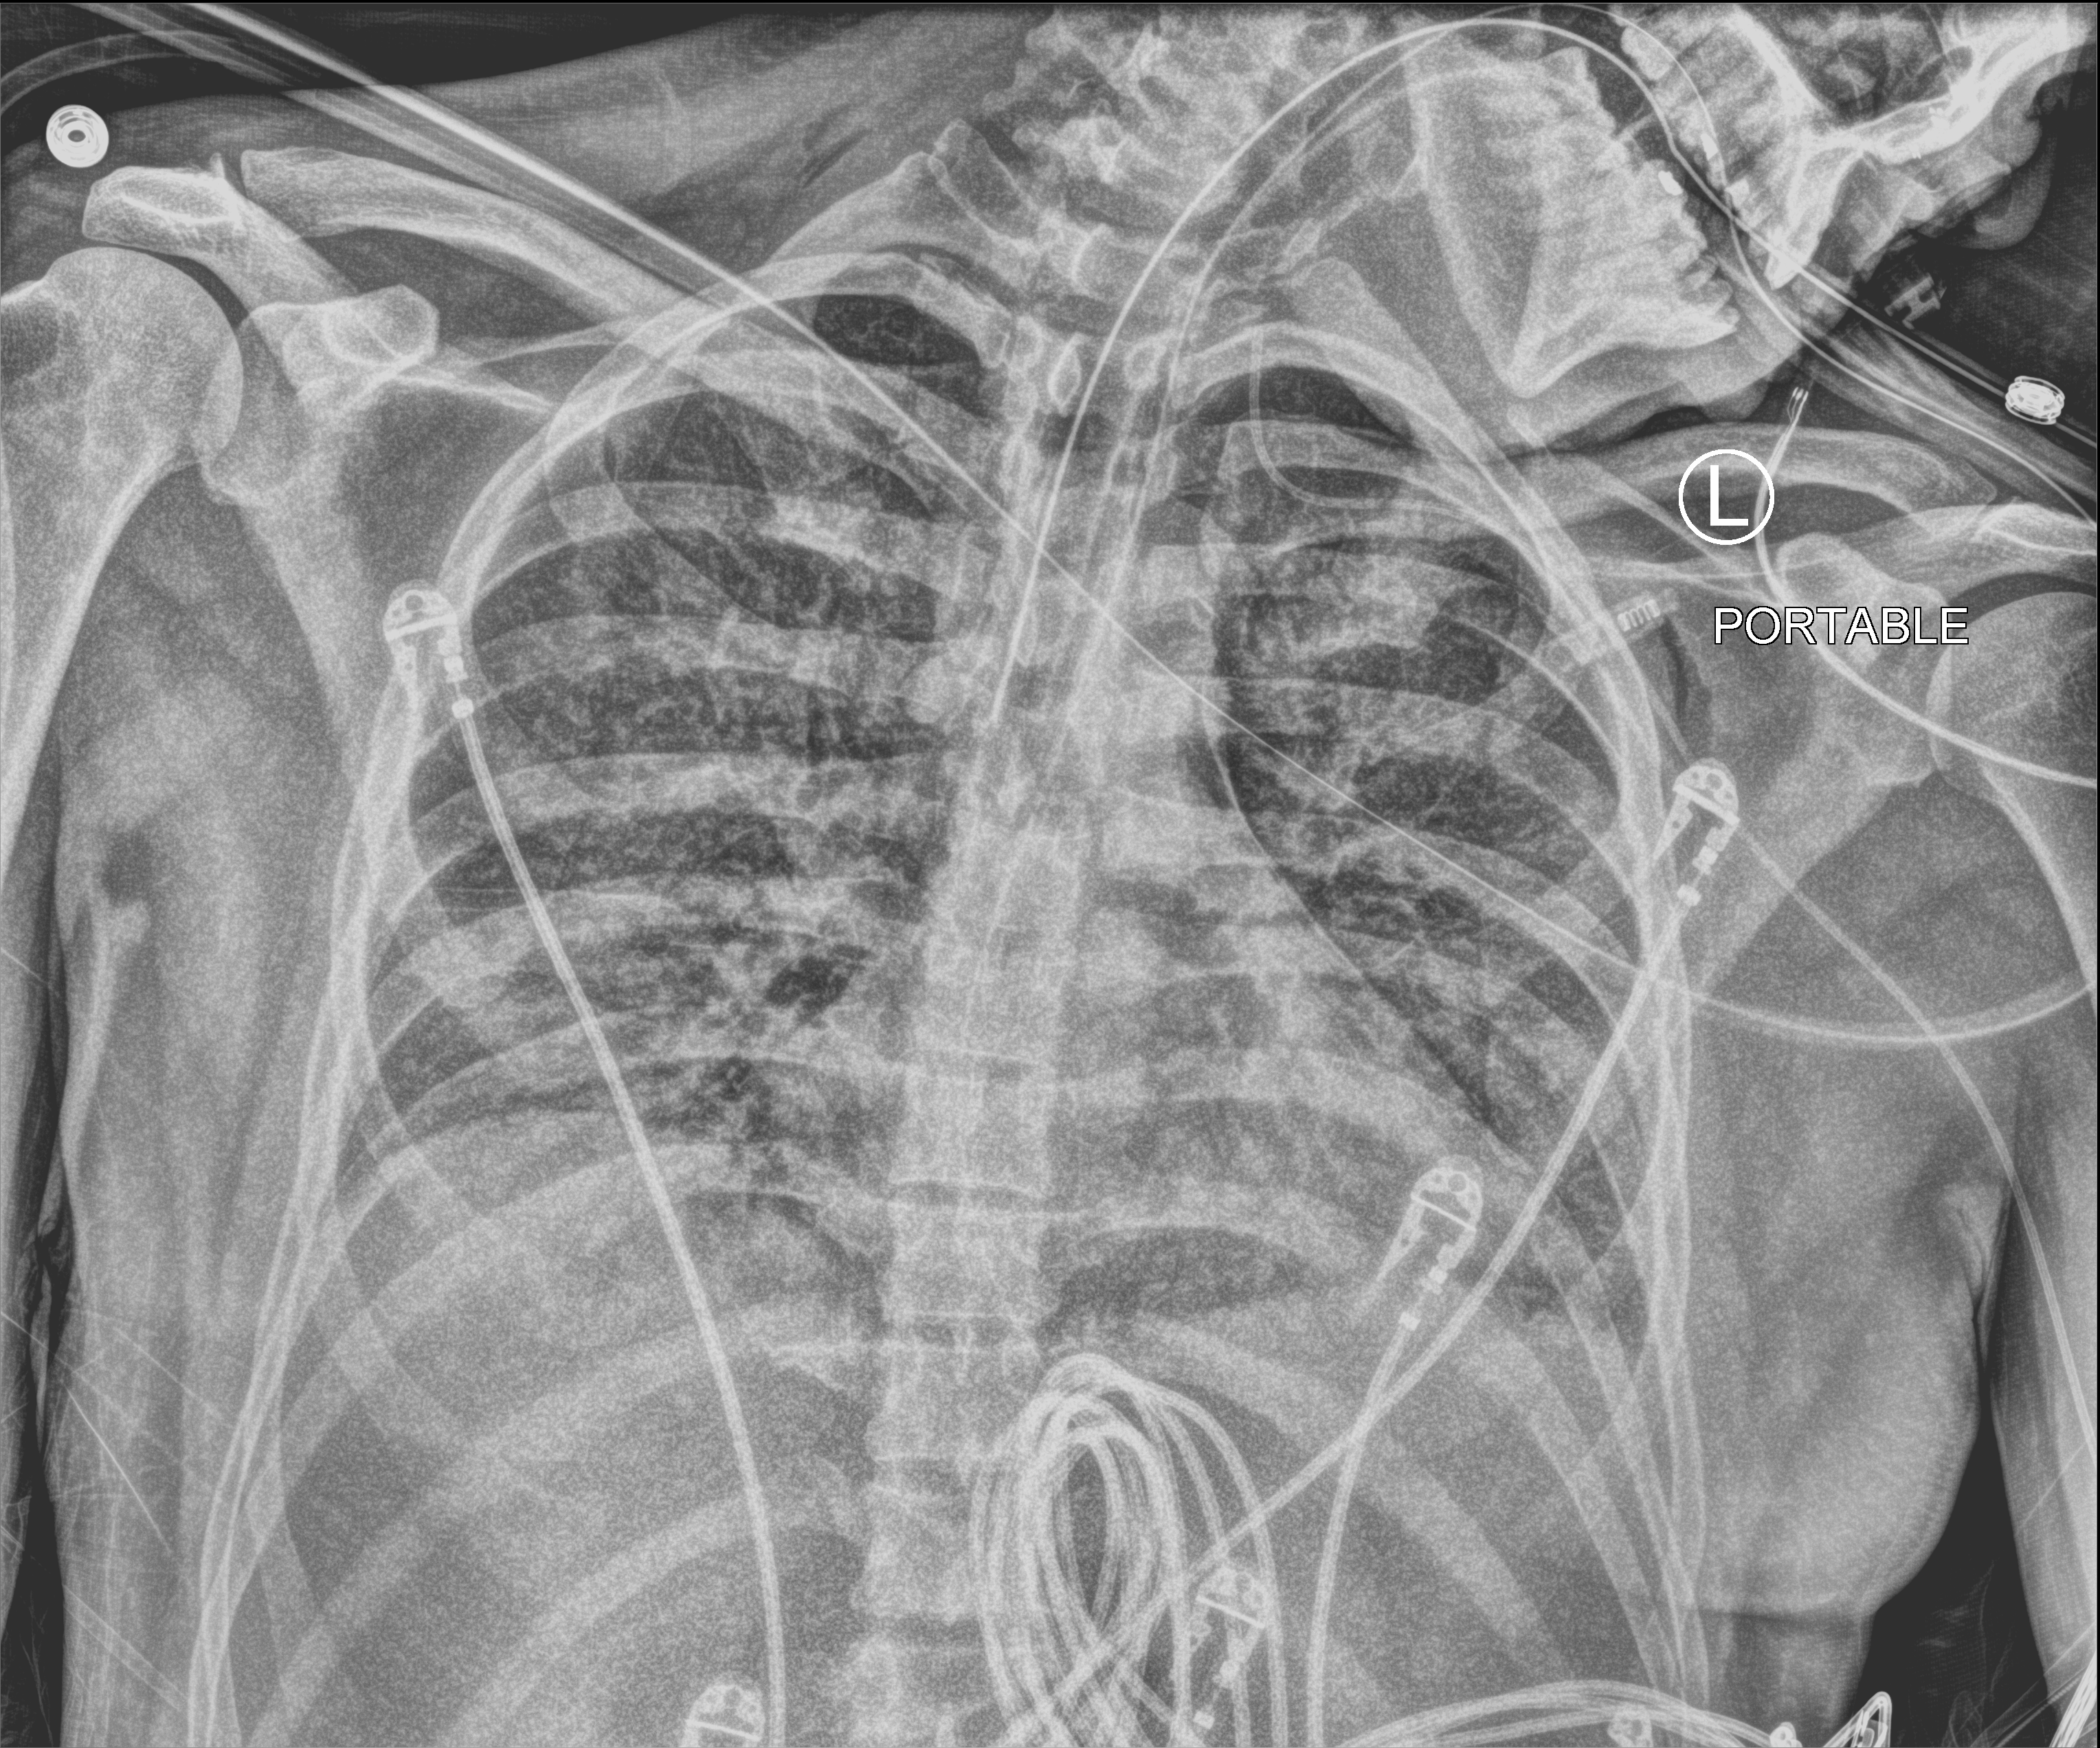
Chest X-ray (portable). Patient hospitalised with COVID-19; male, aged 18–59 years.
Hospital-stay facts (about this admission, not read from this image; timing relative to this image not recorded): admitted to intensive care during this hospital stay: yes.